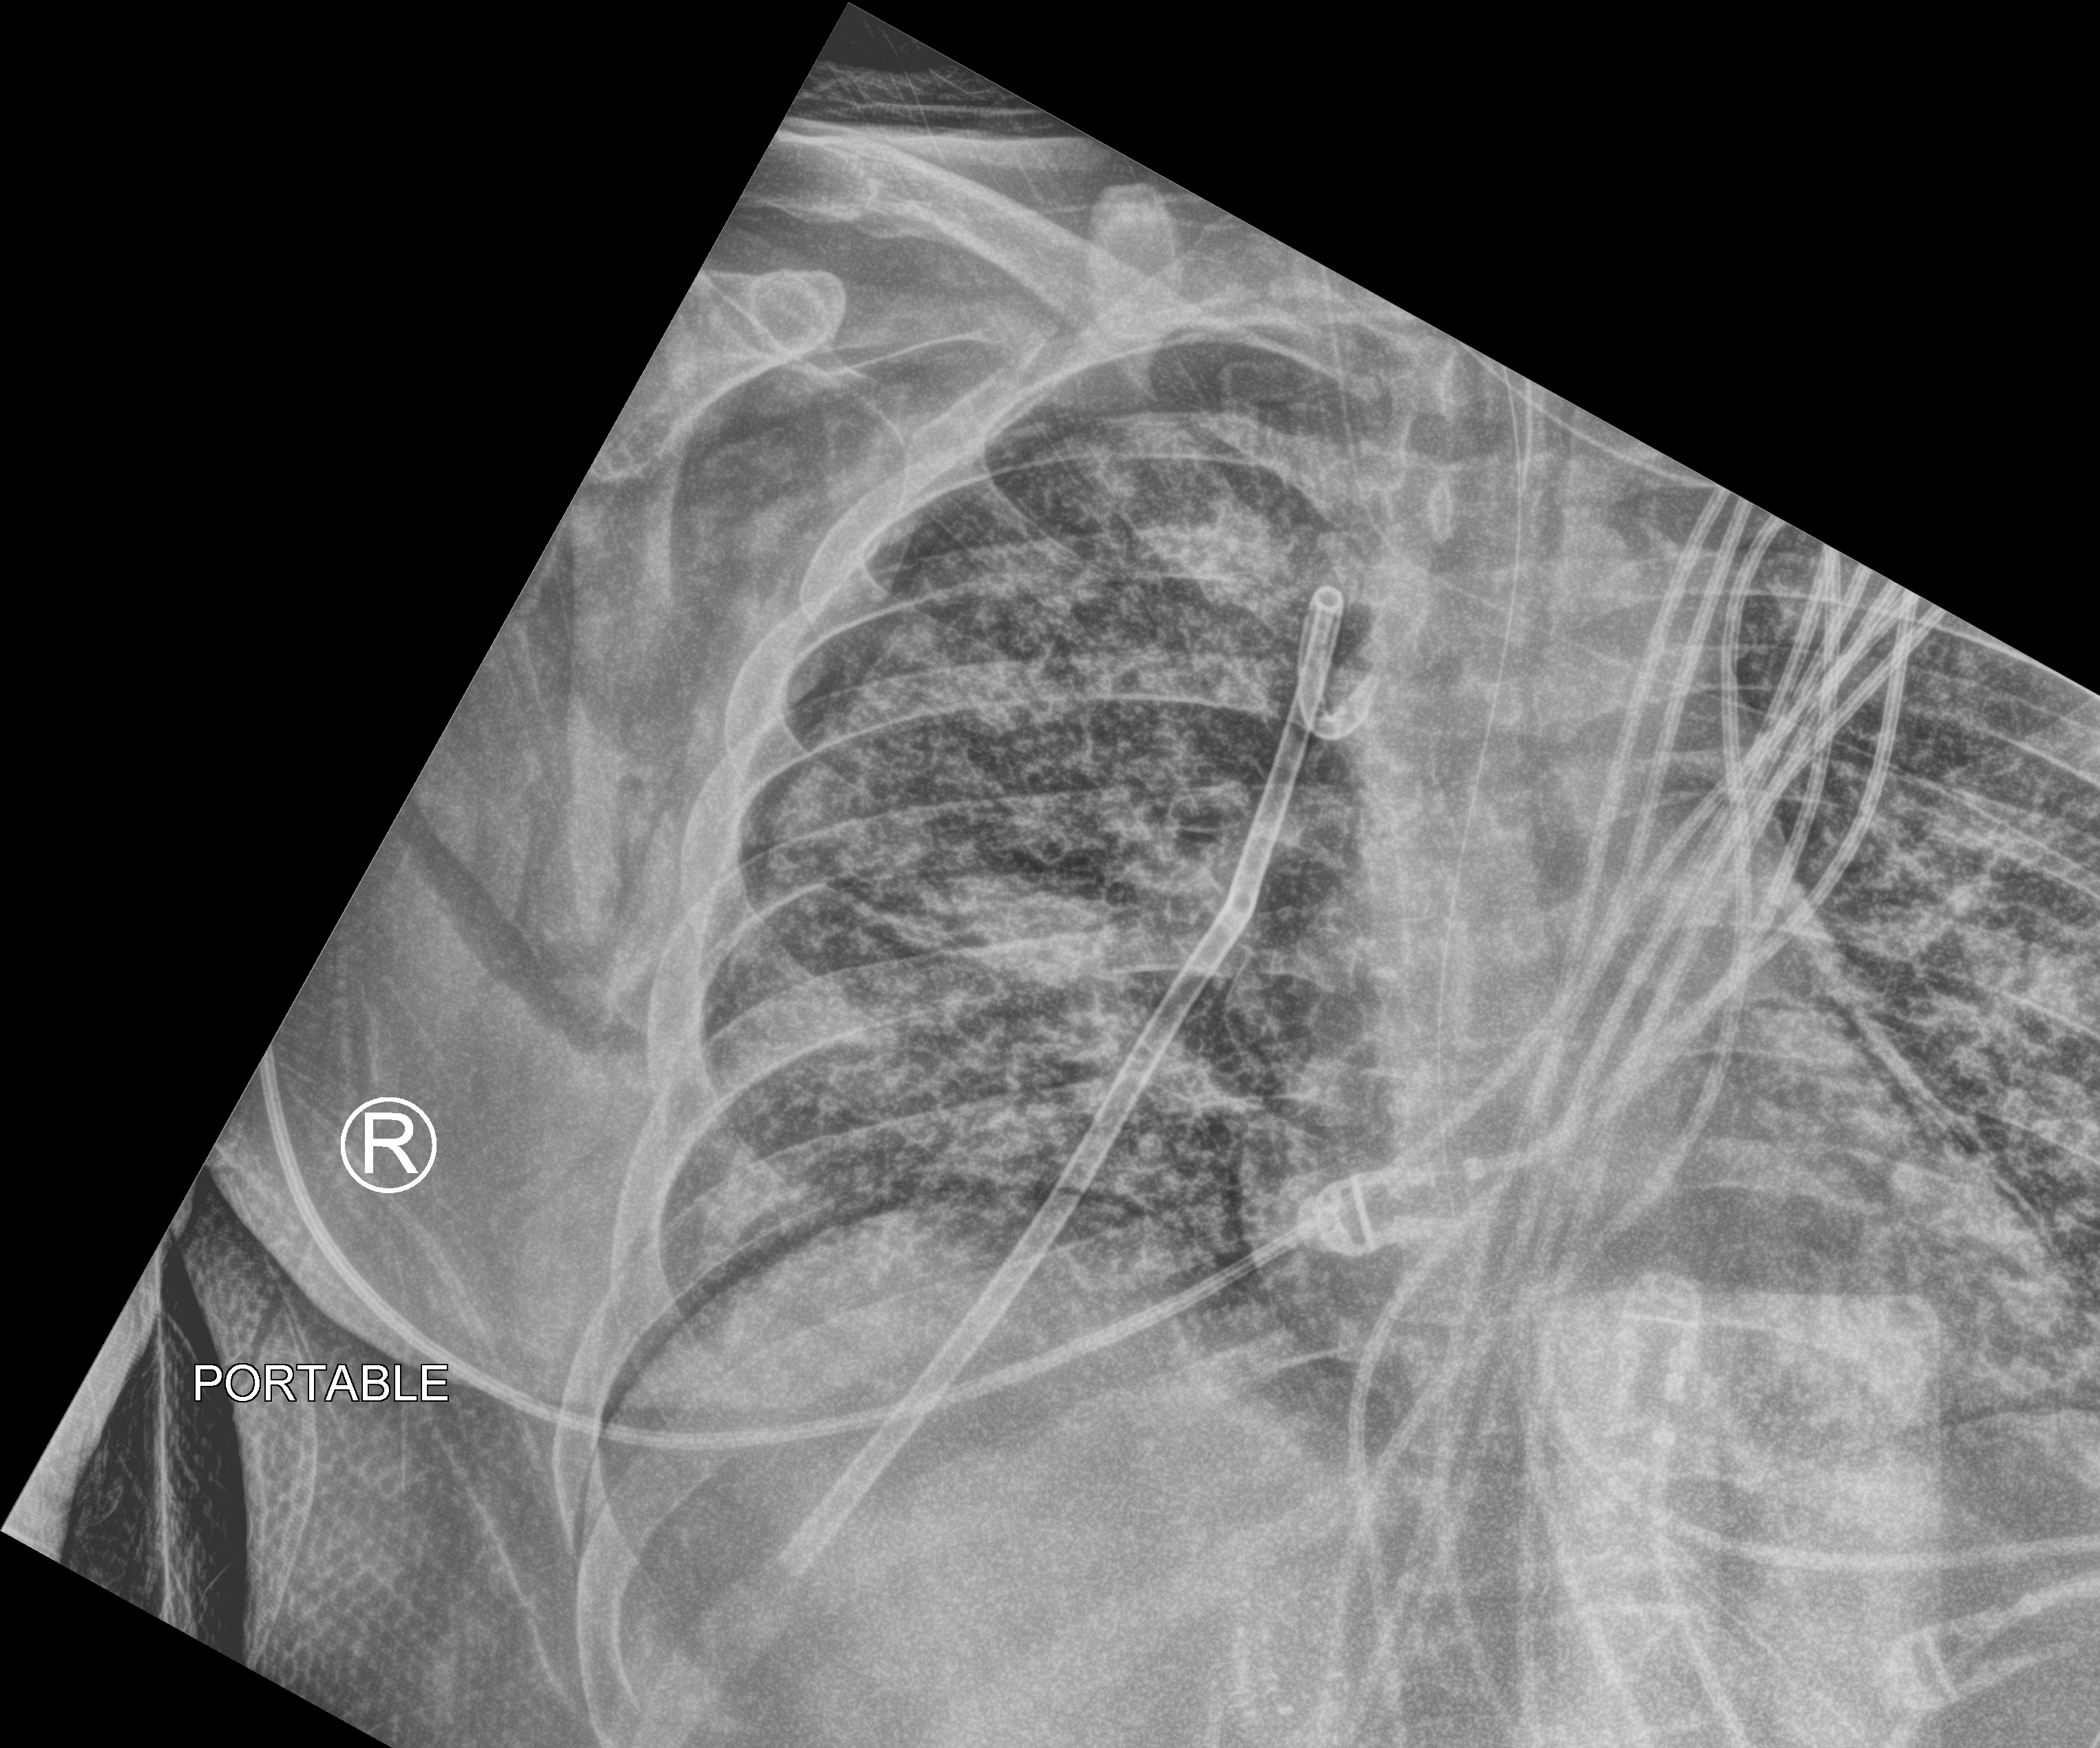
Bedside chest radiograph (computed radiography); anteroposterior (AP) projection. Patient hospitalised with COVID-19, aged 18–59 years.
From the hospital-stay record, not from the radiograph (when in the stay this image was taken is not recorded):
- length of hospital stay: 31 days
- admitted to intensive care during this hospital stay: yes
- mechanically ventilated during this hospital stay: yes